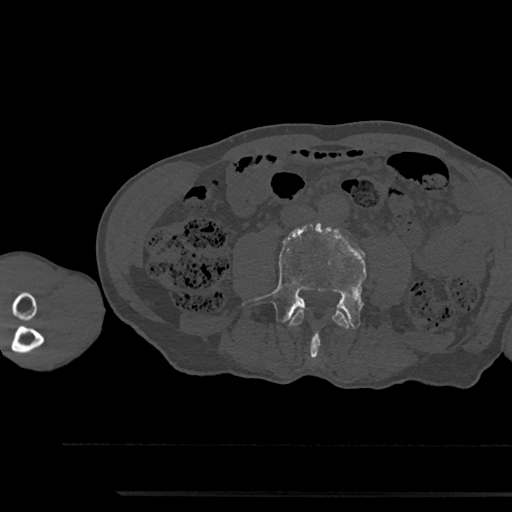
CT including the spine, one axial slice; position 433 of 797 along the scan axis; 120 kVp; bone window (W 1800 / L 400 HU); 0.5 mm slice thickness; 512 × 512 image matrix, field of view 367 × 367 mm. Patient: male, 79 years. From the clinical record (not read from this slice): primary cancer: prostate.
Annotated regions visible in this slice (semi-automatically segmented with operator editing):
- L3 vertebra: bounding box <290,309,350,329> (left, top, right, bottom; pixels)
- L4 vertebra: <243,224,366,357>